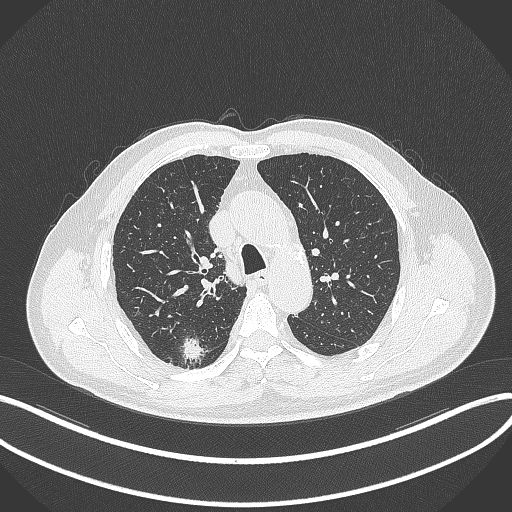
Chest CT, one axial slice; position 264 of 359 along the scan axis; 120 kVp; lung window (W 1500 / L -600 HU); 512 × 512 image matrix, field of view 400 × 400 mm. Patient: male, 69 years. From the clinical record (not read from this slice): clinical TNM (as recorded): T1b N0 M0; histopathological grade: G2-3.
Structures marked on this image (bounding box drawn by a radiologist):
- lung tumour (recorded histology: adenocarcinoma): box from (x=179, y=329) to (x=206, y=366) px